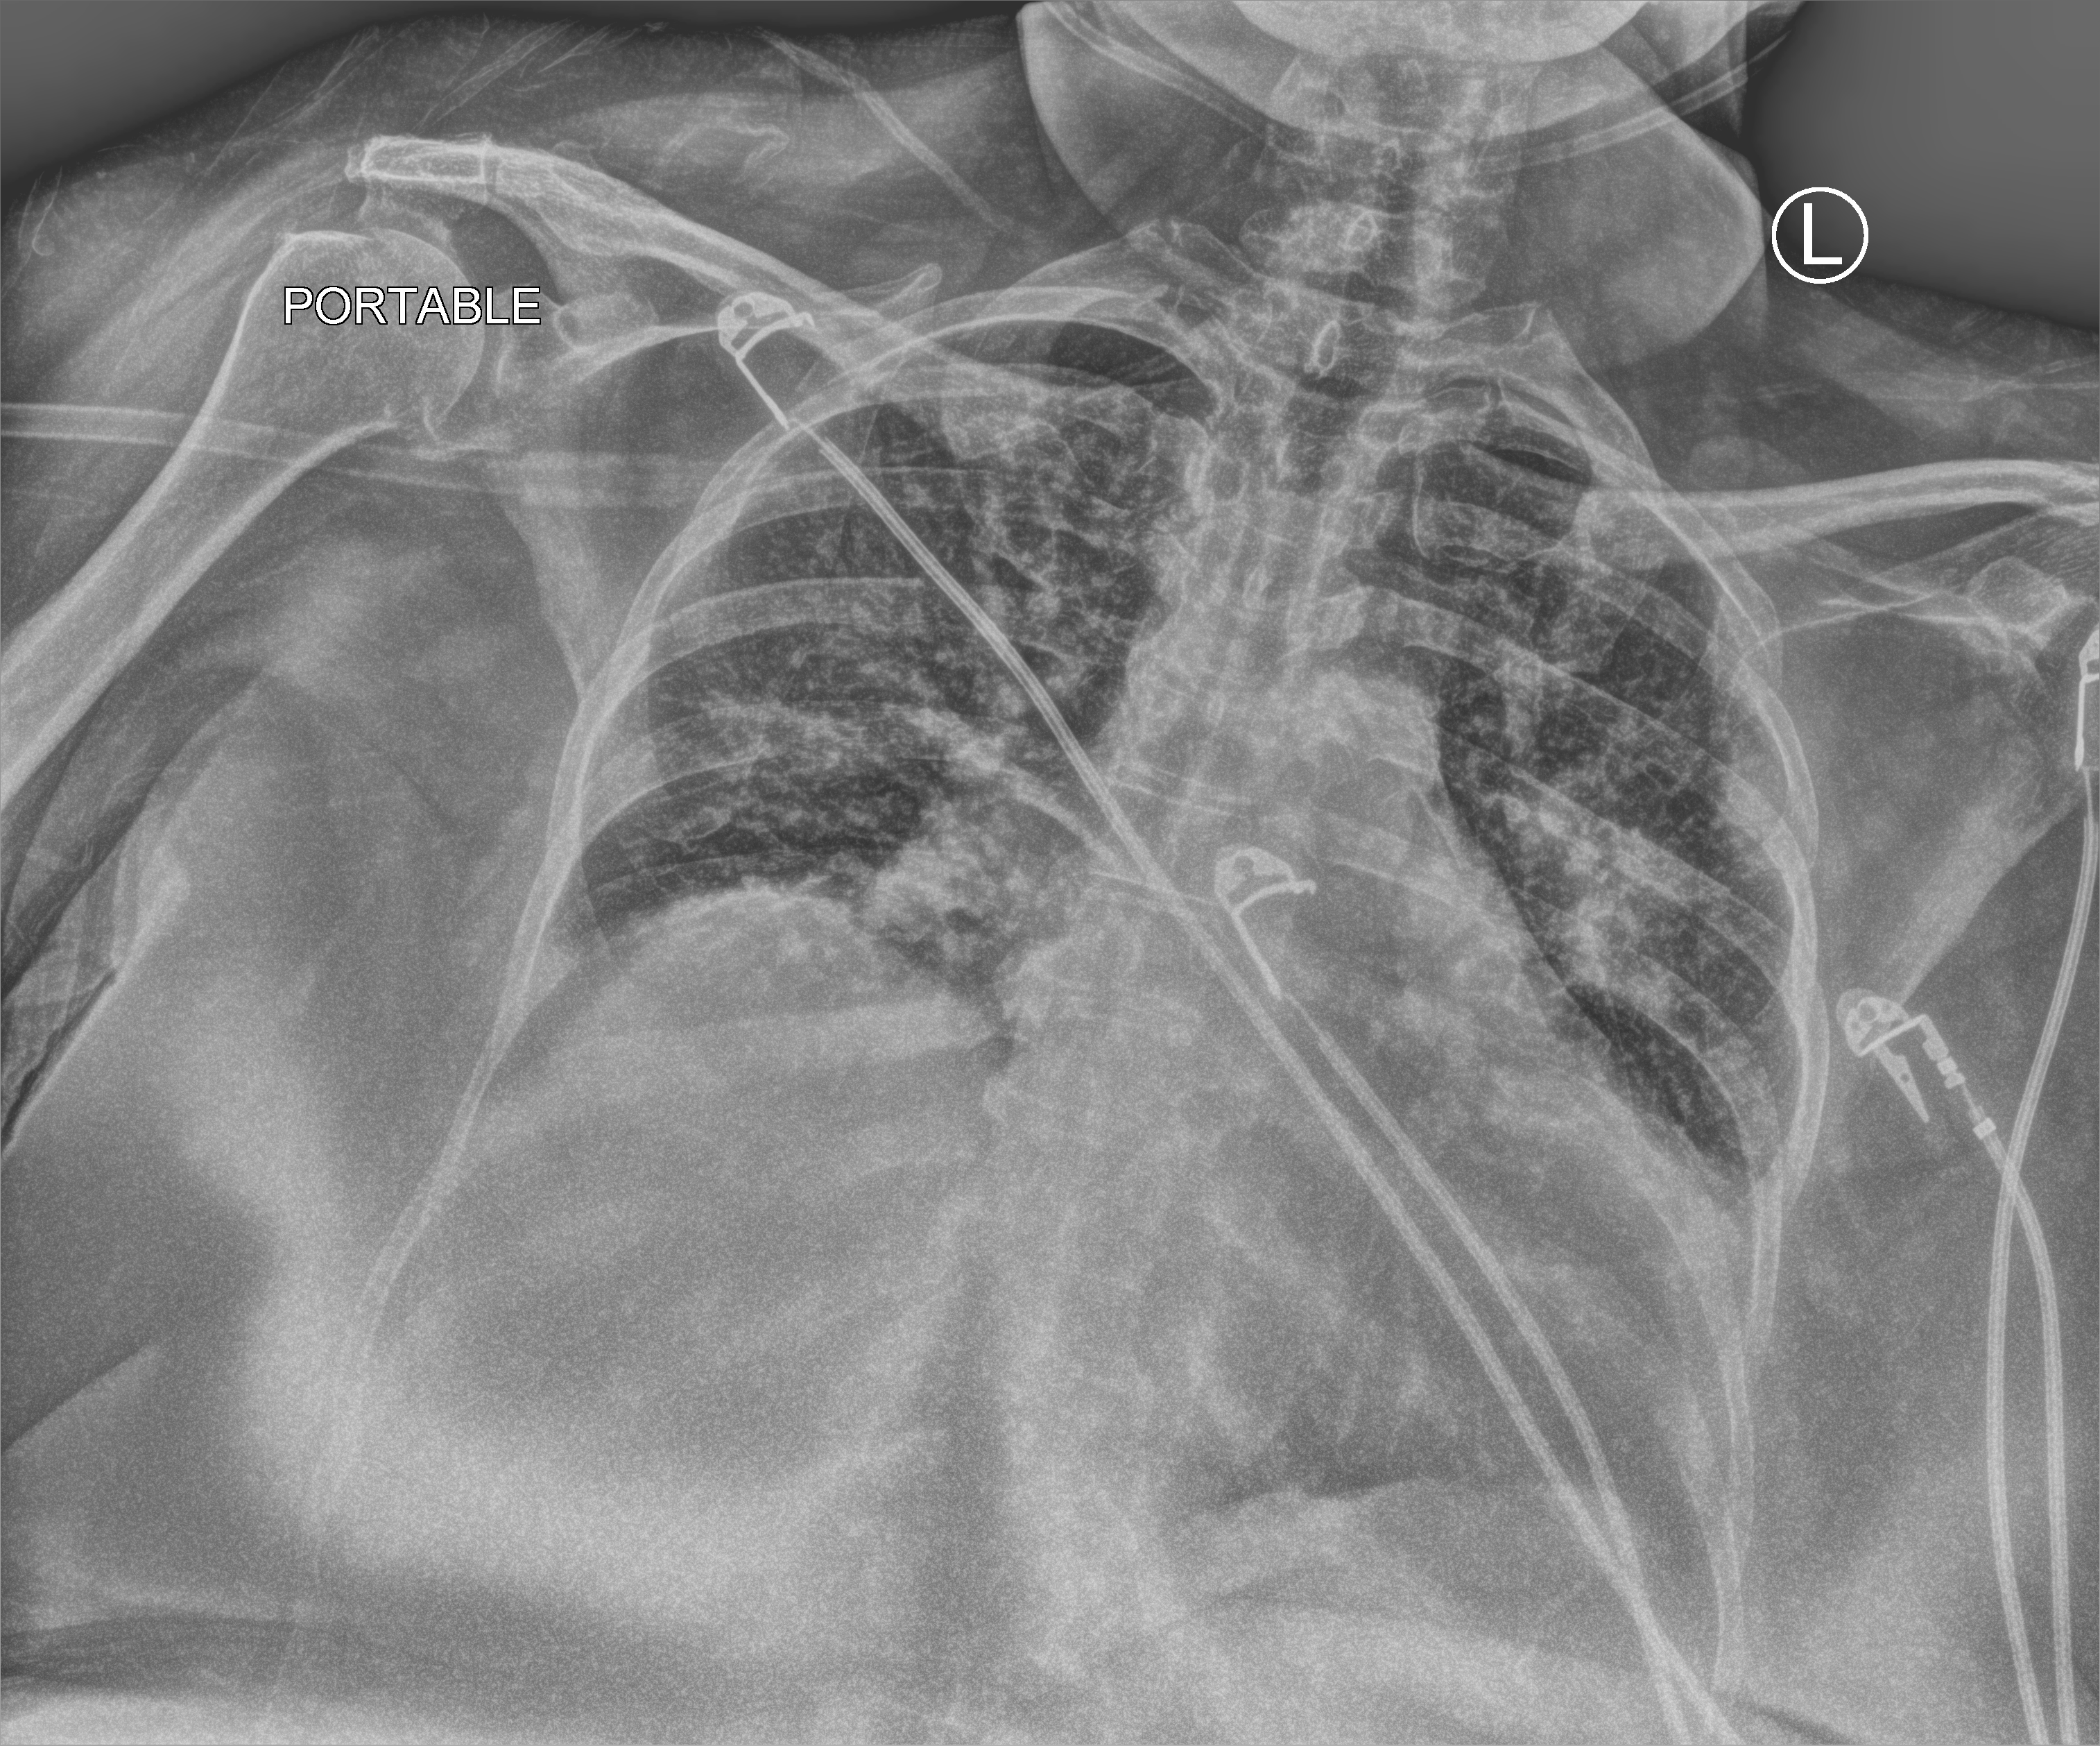
Portable chest radiograph; anteroposterior (AP) projection. Patient hospitalised with COVID-19; female, aged 60–74 years.
From the hospital-stay record, not from the radiograph (when in the stay this image was taken is not recorded):
- smoking status (admission record): never
- COPD (admission record): no